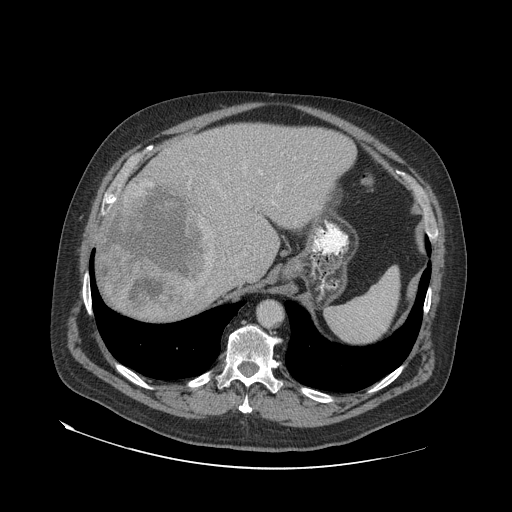
Contrast-enhanced abdominal CT (liver protocol), one axial slice. Slice 53 of 79 in the series (ordered by position). Soft-tissue window (W 400 / L 40 HU). 512 × 512 image matrix, field of view 480 × 480 mm. Case-level facts recorded for this patient, not image findings: diagnosis: hepatocellular carcinoma (patient treated with transarterial chemoembolisation; whether this scan precedes or follows treatment is not stated here); TNM stage (as recorded): Stage-IVA; Child-Pugh class: A; tumour differentiation: well differentiated.
Annotated regions visible in this slice (semi-automatic segmentation, software-assisted and operator-edited):
- abdominal aorta: box from (x=259, y=302) to (x=282, y=327) px
- liver parenchyma outside the tumour (the mass and vessels are separate outlines, so this box may not span the whole liver): (x=98, y=124)–(x=356, y=314)
- mass: (x=98, y=181)–(x=218, y=321)
- liver vessels: (x=259, y=170)–(x=274, y=203)